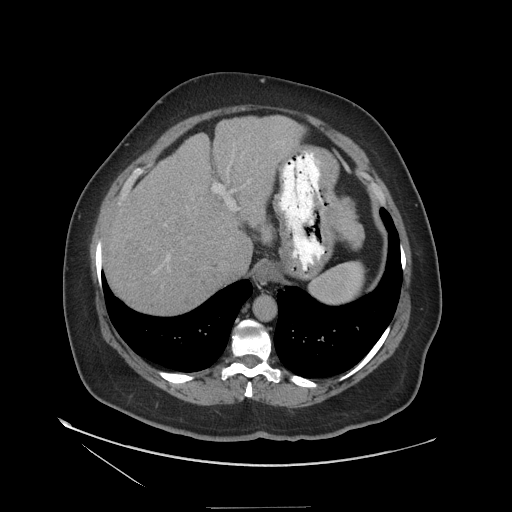
Contrast-enhanced abdominal CT (liver protocol), one axial slice. Slice 92 of 127 in the series (ordered by position). 140 kVp. Soft-tissue window (W 400 / L 40 HU). 2.5 mm slice thickness. 512 × 512 image matrix, field of view 480 × 480 mm. From the clinical record (not read from this slice): diagnosis: hepatocellular carcinoma (patient treated with transarterial chemoembolisation; whether this scan precedes or follows treatment is not stated here); TNM stage (as recorded): Stage-II; Child-Pugh class: A; tumour differentiation: well differentiated.
Outlined on this slice (semi-automatic segmentation, software-assisted and operator-edited):
- abdominal aorta: bounding box (x1, y1, x2, y2) in pixels: (253, 296, 275, 322)
- liver parenchyma outside the tumour (the mass and vessels are separate outlines, so this box may not span the whole liver): (104, 116, 302, 314)
- mass: (123, 234, 142, 256)
- liver vessels: (124, 185, 233, 207)